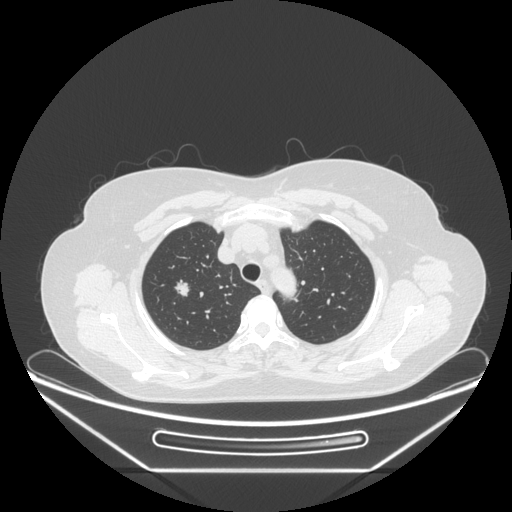
Chest CT, one axial slice. 120 kVp. Lung window (W 1500 / L -600 HU). 1.25 mm slice thickness. 512 × 512 image matrix, field of view 433 × 433 mm. Female patient, age 60 years. From the clinical record (not read from this slice): clinical TNM (as recorded): T1c N0 M0.
Structures marked on this image (rectangle marked by the reading radiologist):
- lung tumour (recorded histology: adenocarcinoma): bounding box <172,273,195,305> (left, top, right, bottom; pixels)